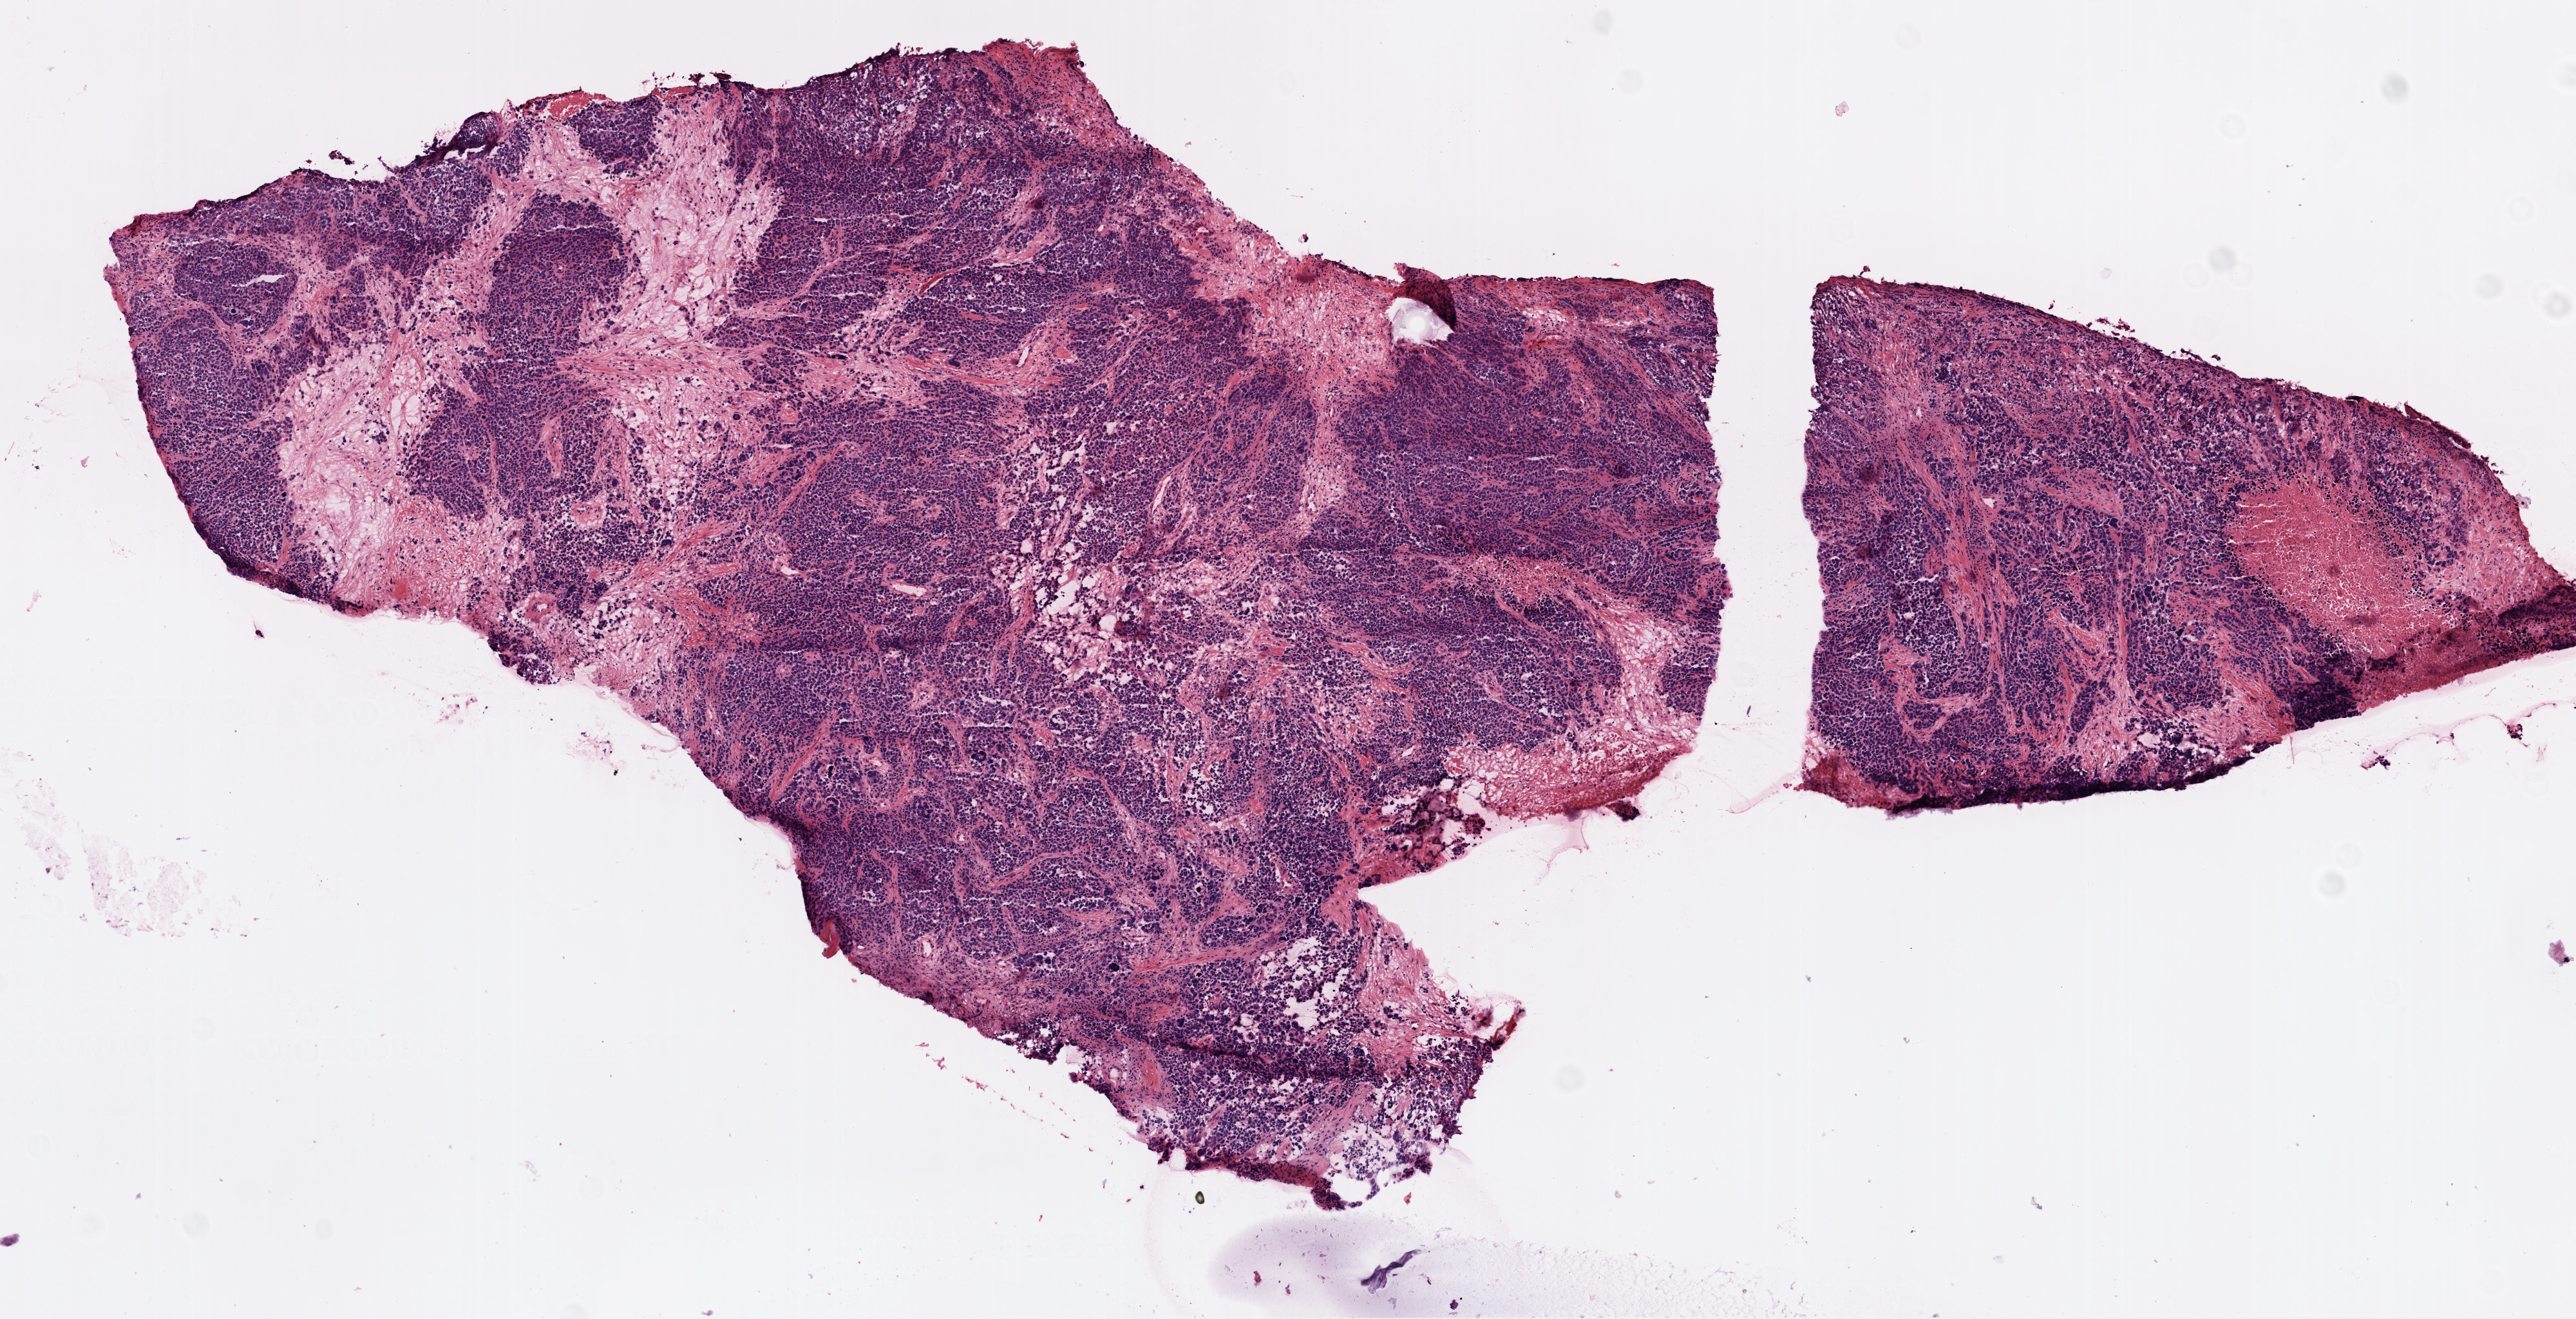
Whole-slide histology image, H&E-stained, whole scanned area (about 8.0 x 4.1 mm, slide scanned at 20x) shown as a low-resolution overview, frozen section, sample: primary tumour, ovary. Patient: female, age at initial diagnosis 65 years.
Diagnosis: Serous cystadenocarcinoma, NOS.